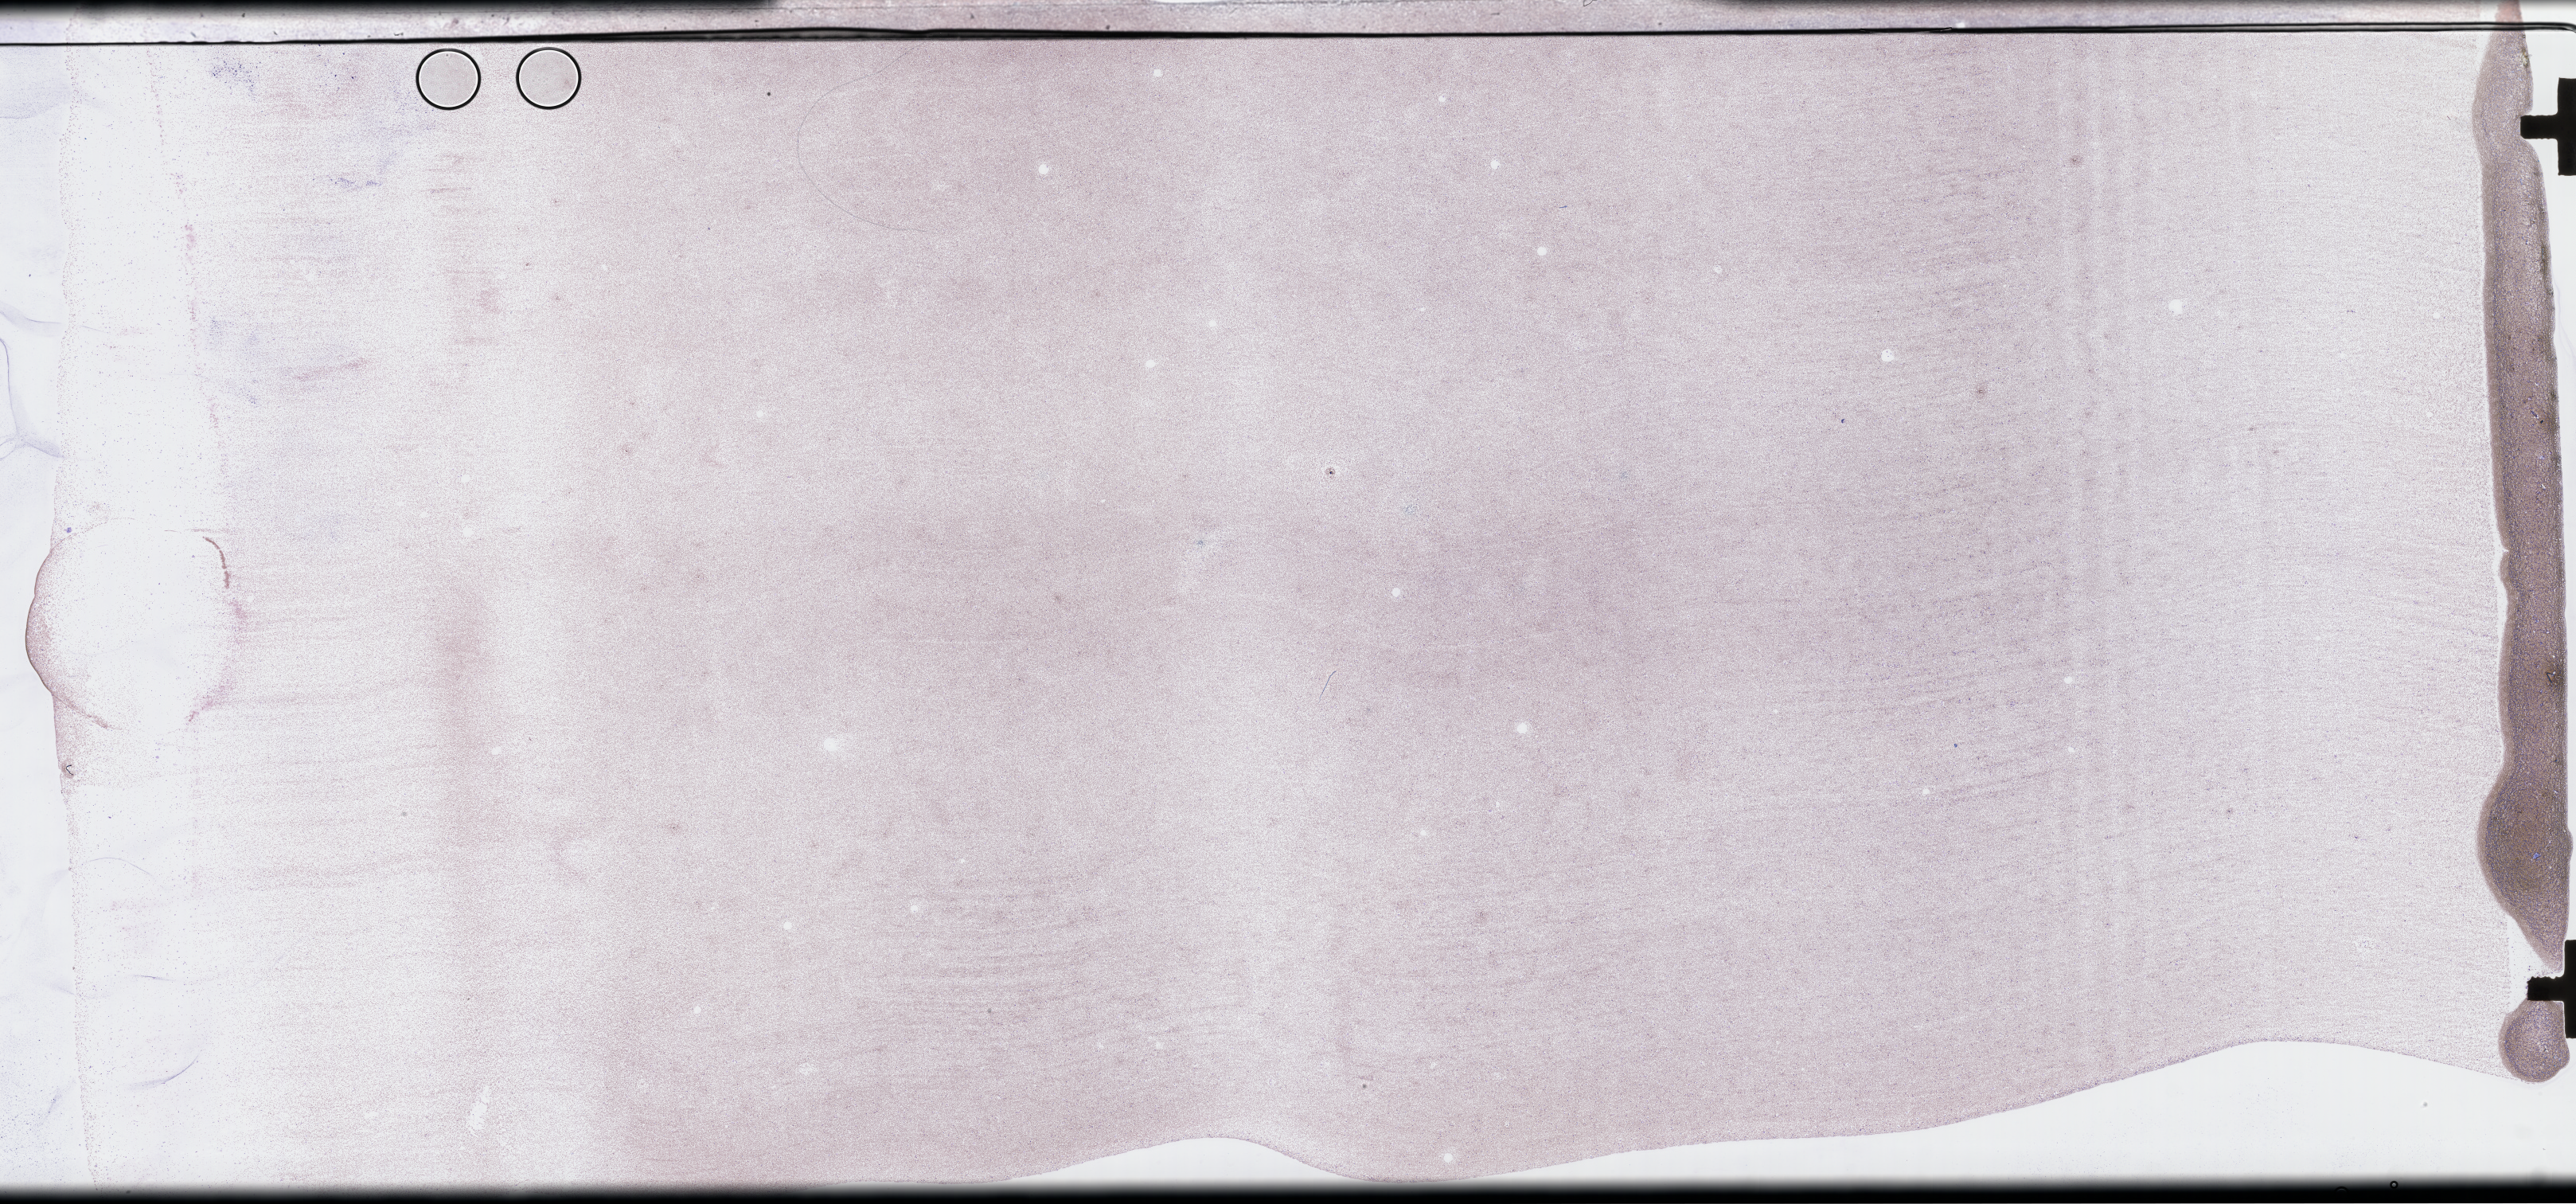
Wright–Giemsa-stained bone marrow smear, whole-slide image, low-resolution overview of the scanned area, about 52.3 x 24.4 mm; smear from an EDTA sample. Patient sex: male.
Patient diagnosis: Plasma Cell Myeloma.